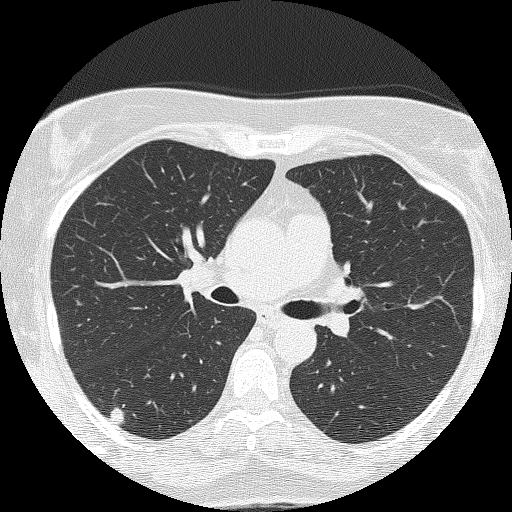
Axial slice from a low-dose chest CT screening exam; second annual screen; lung window (W 1500 / L -600 HU); lung (sharp) reconstruction kernel (FC51). Female participant, aged 58 years at enrolment.
Lesion marked by an expert reader, box from (x=89, y=395) to (x=142, y=433) px. The screening reader recorded 2 non-calcified nodules or masses ≥4 mm on this exam (right upper lobe, right upper lobe); which of them this box marks is not recorded.